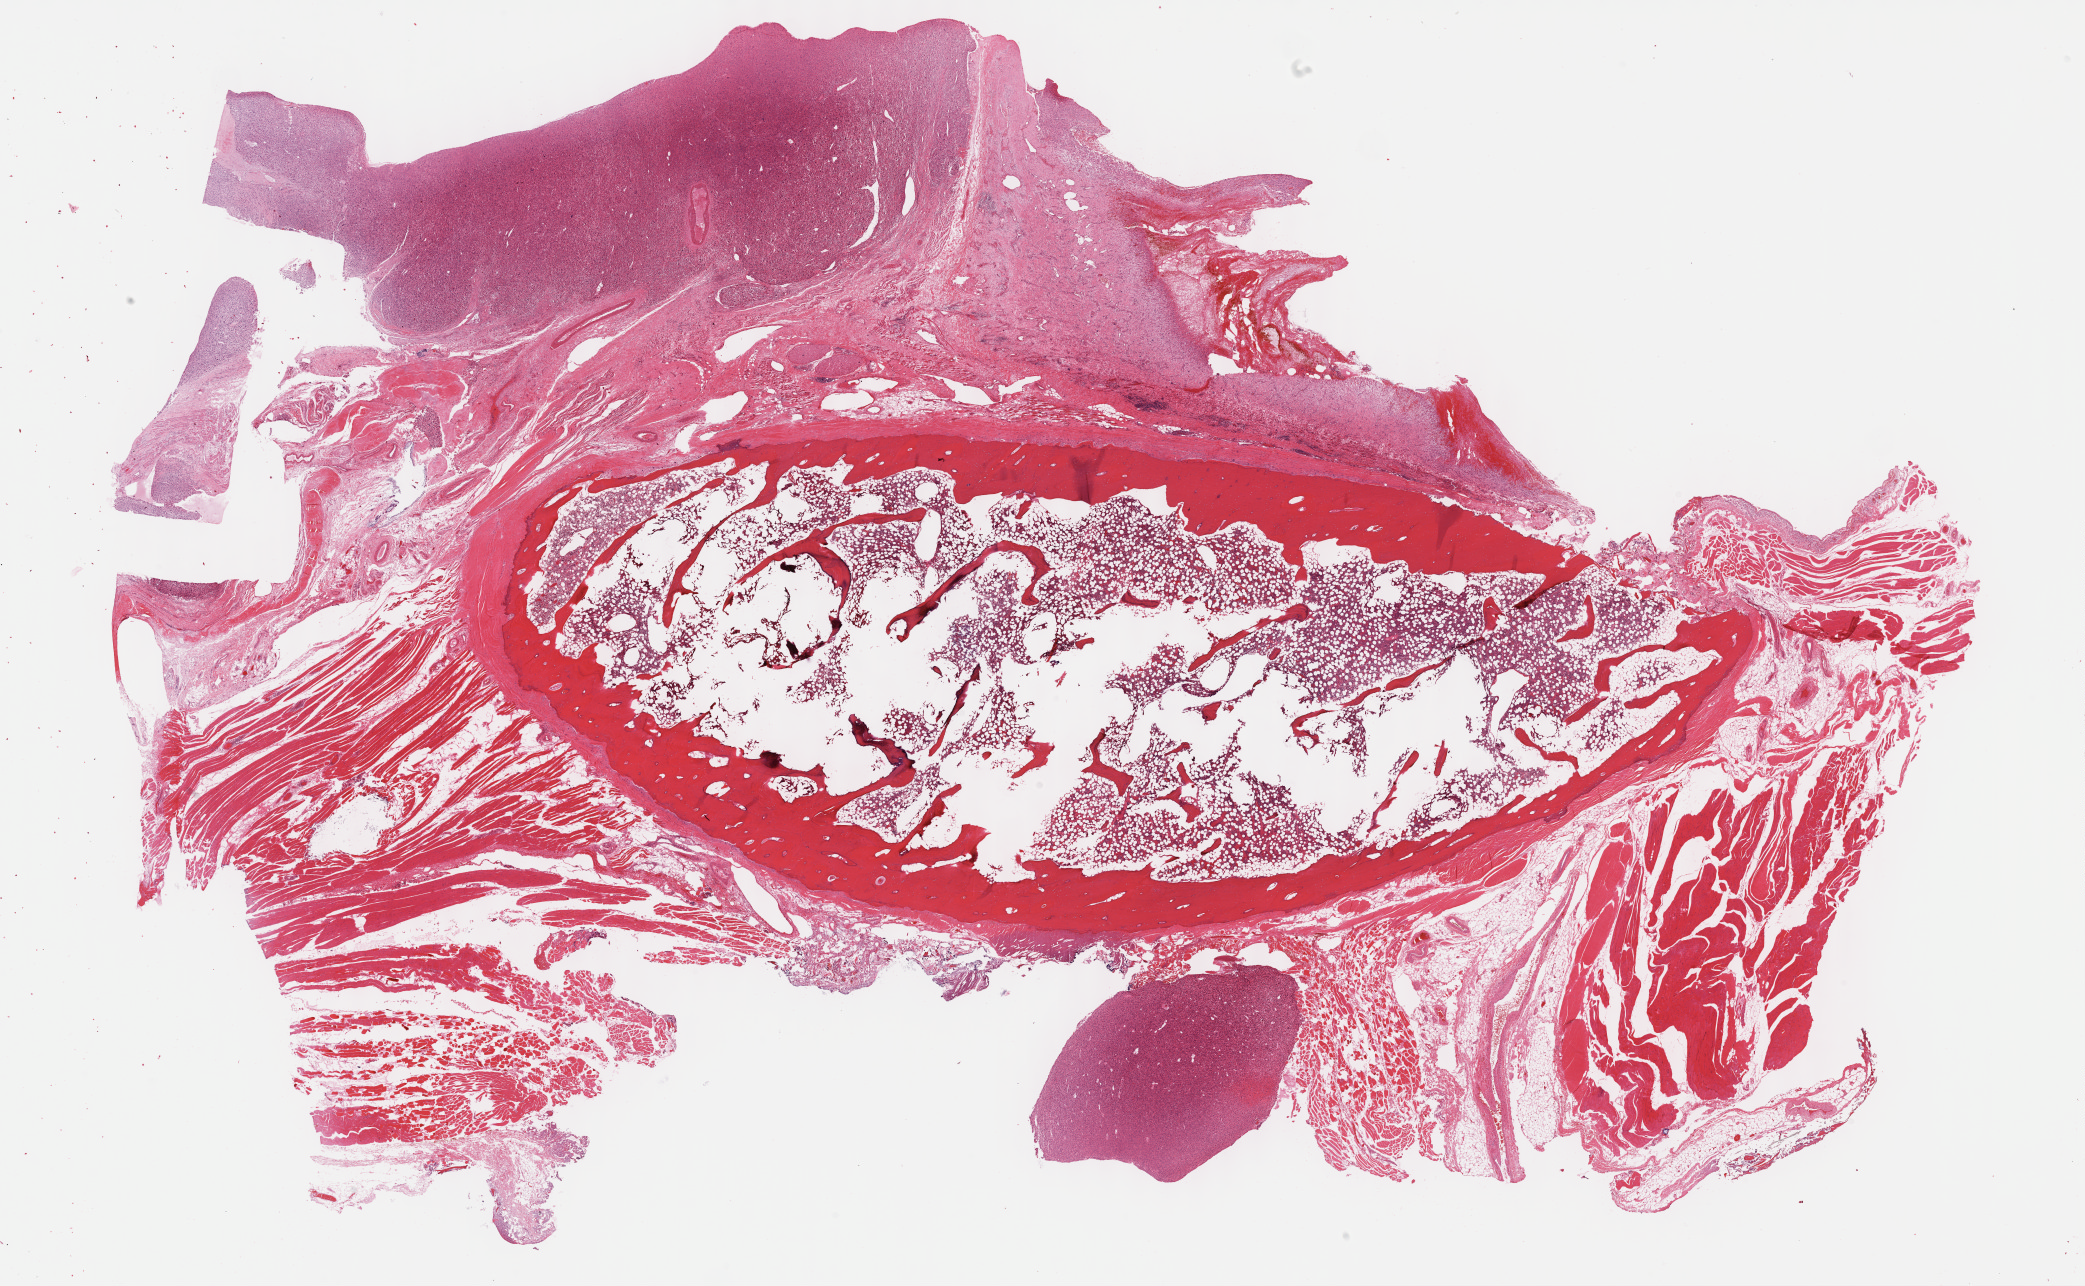
Whole-slide histology image, H&E-stained, low-resolution overview of the scanned area, about 33.7 x 20.8 mm (slide scanned at 40x). Formalin-fixed paraffin-embedded (FFPE) diagnostic section. Sample: primary tumour, connective, subcutaneous and other soft tissues. Patient: female, age at initial diagnosis 49 years.
Diagnosis: Undifferentiated sarcoma (connective, subcutaneous and other soft tissues of thorax).